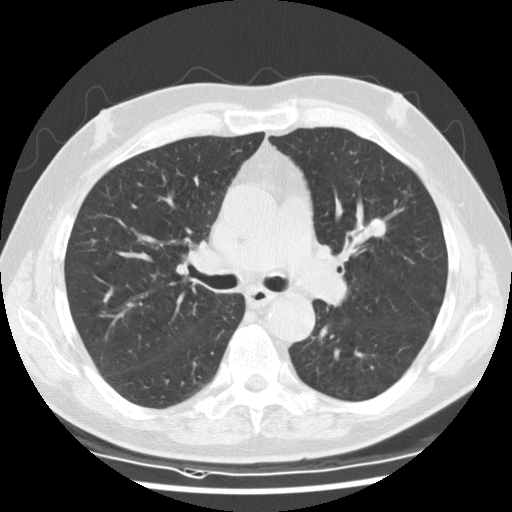
Axial slice from a low-dose chest CT screening exam; first (baseline) screen; lung window (W 1500 / L -600 HU); standard (soft-tissue) reconstruction kernel (STANDARD); slice 59 of 135 in the series. Male, age 73 years at enrolment.
- Expert reader's lesion annotation, bounding box (x1, y1, x2, y2) in pixels: (340, 203, 405, 255).
- Screening reader's record for this exam (one nodule recorded; not confirmed to be the boxed lesion): non-calcified nodule or mass ≥4 mm, right lower lobe, 13 × 13 mm, smooth margins, soft tissue attenuation.
- Note: the box lies in the patient's left hemithorax on this image, whereas the reader's record names the right lung; they may be different findings.
- Official screen result: positive, change unspecified: nodule(s) >= 4 mm or enlarging nodule(s), mass(es), or other non-specific abnormalities suspicious for lung cancer.